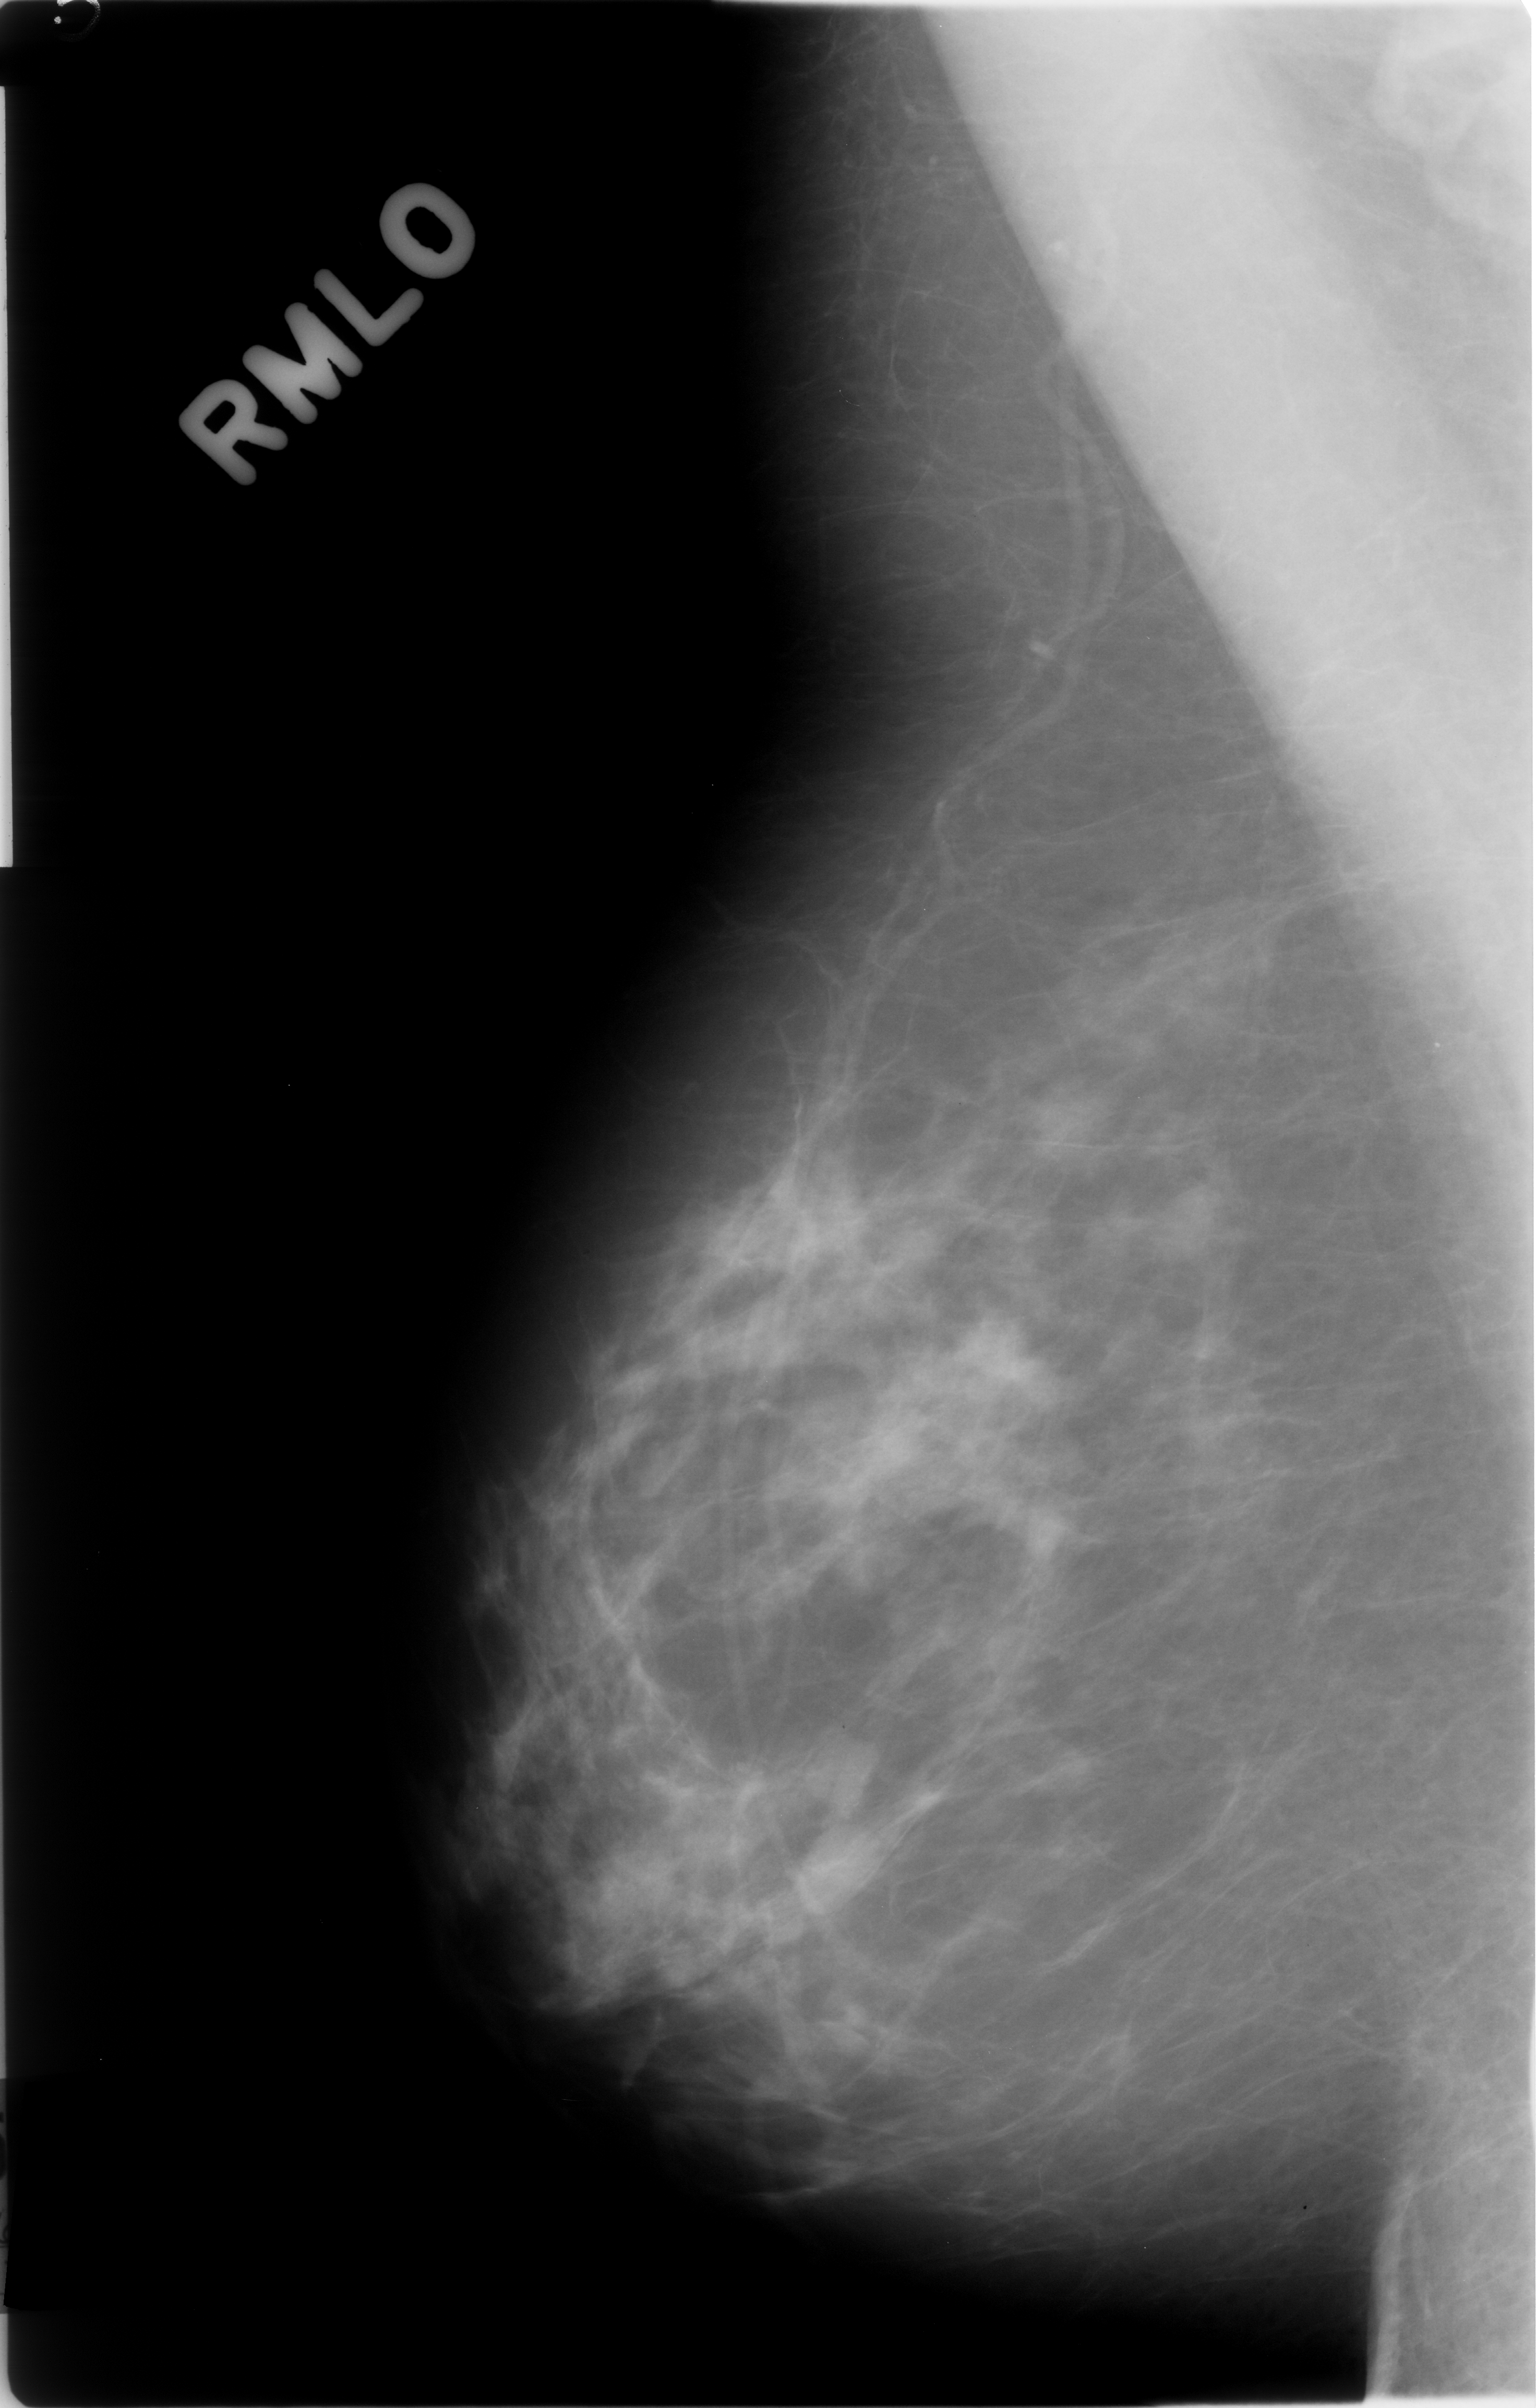
Digitized screen-film mammogram. Right breast. Mediolateral oblique (MLO) view. Breast composition: scattered fibroglandular densities (BI-RADS density category 2 of 4). 1536 × 2408 image matrix.
Marked abnormalities (boxes around the expert regions of interest):
- mass, shape oval, margins circumscribed; BI-RADS assessment category 3; subtlety rating 4 on a 1 (subtle) to 5 (obvious) scale; pathology result (as recorded, not read from the image): benign: box from (x=770, y=1745) to (x=919, y=1917) px